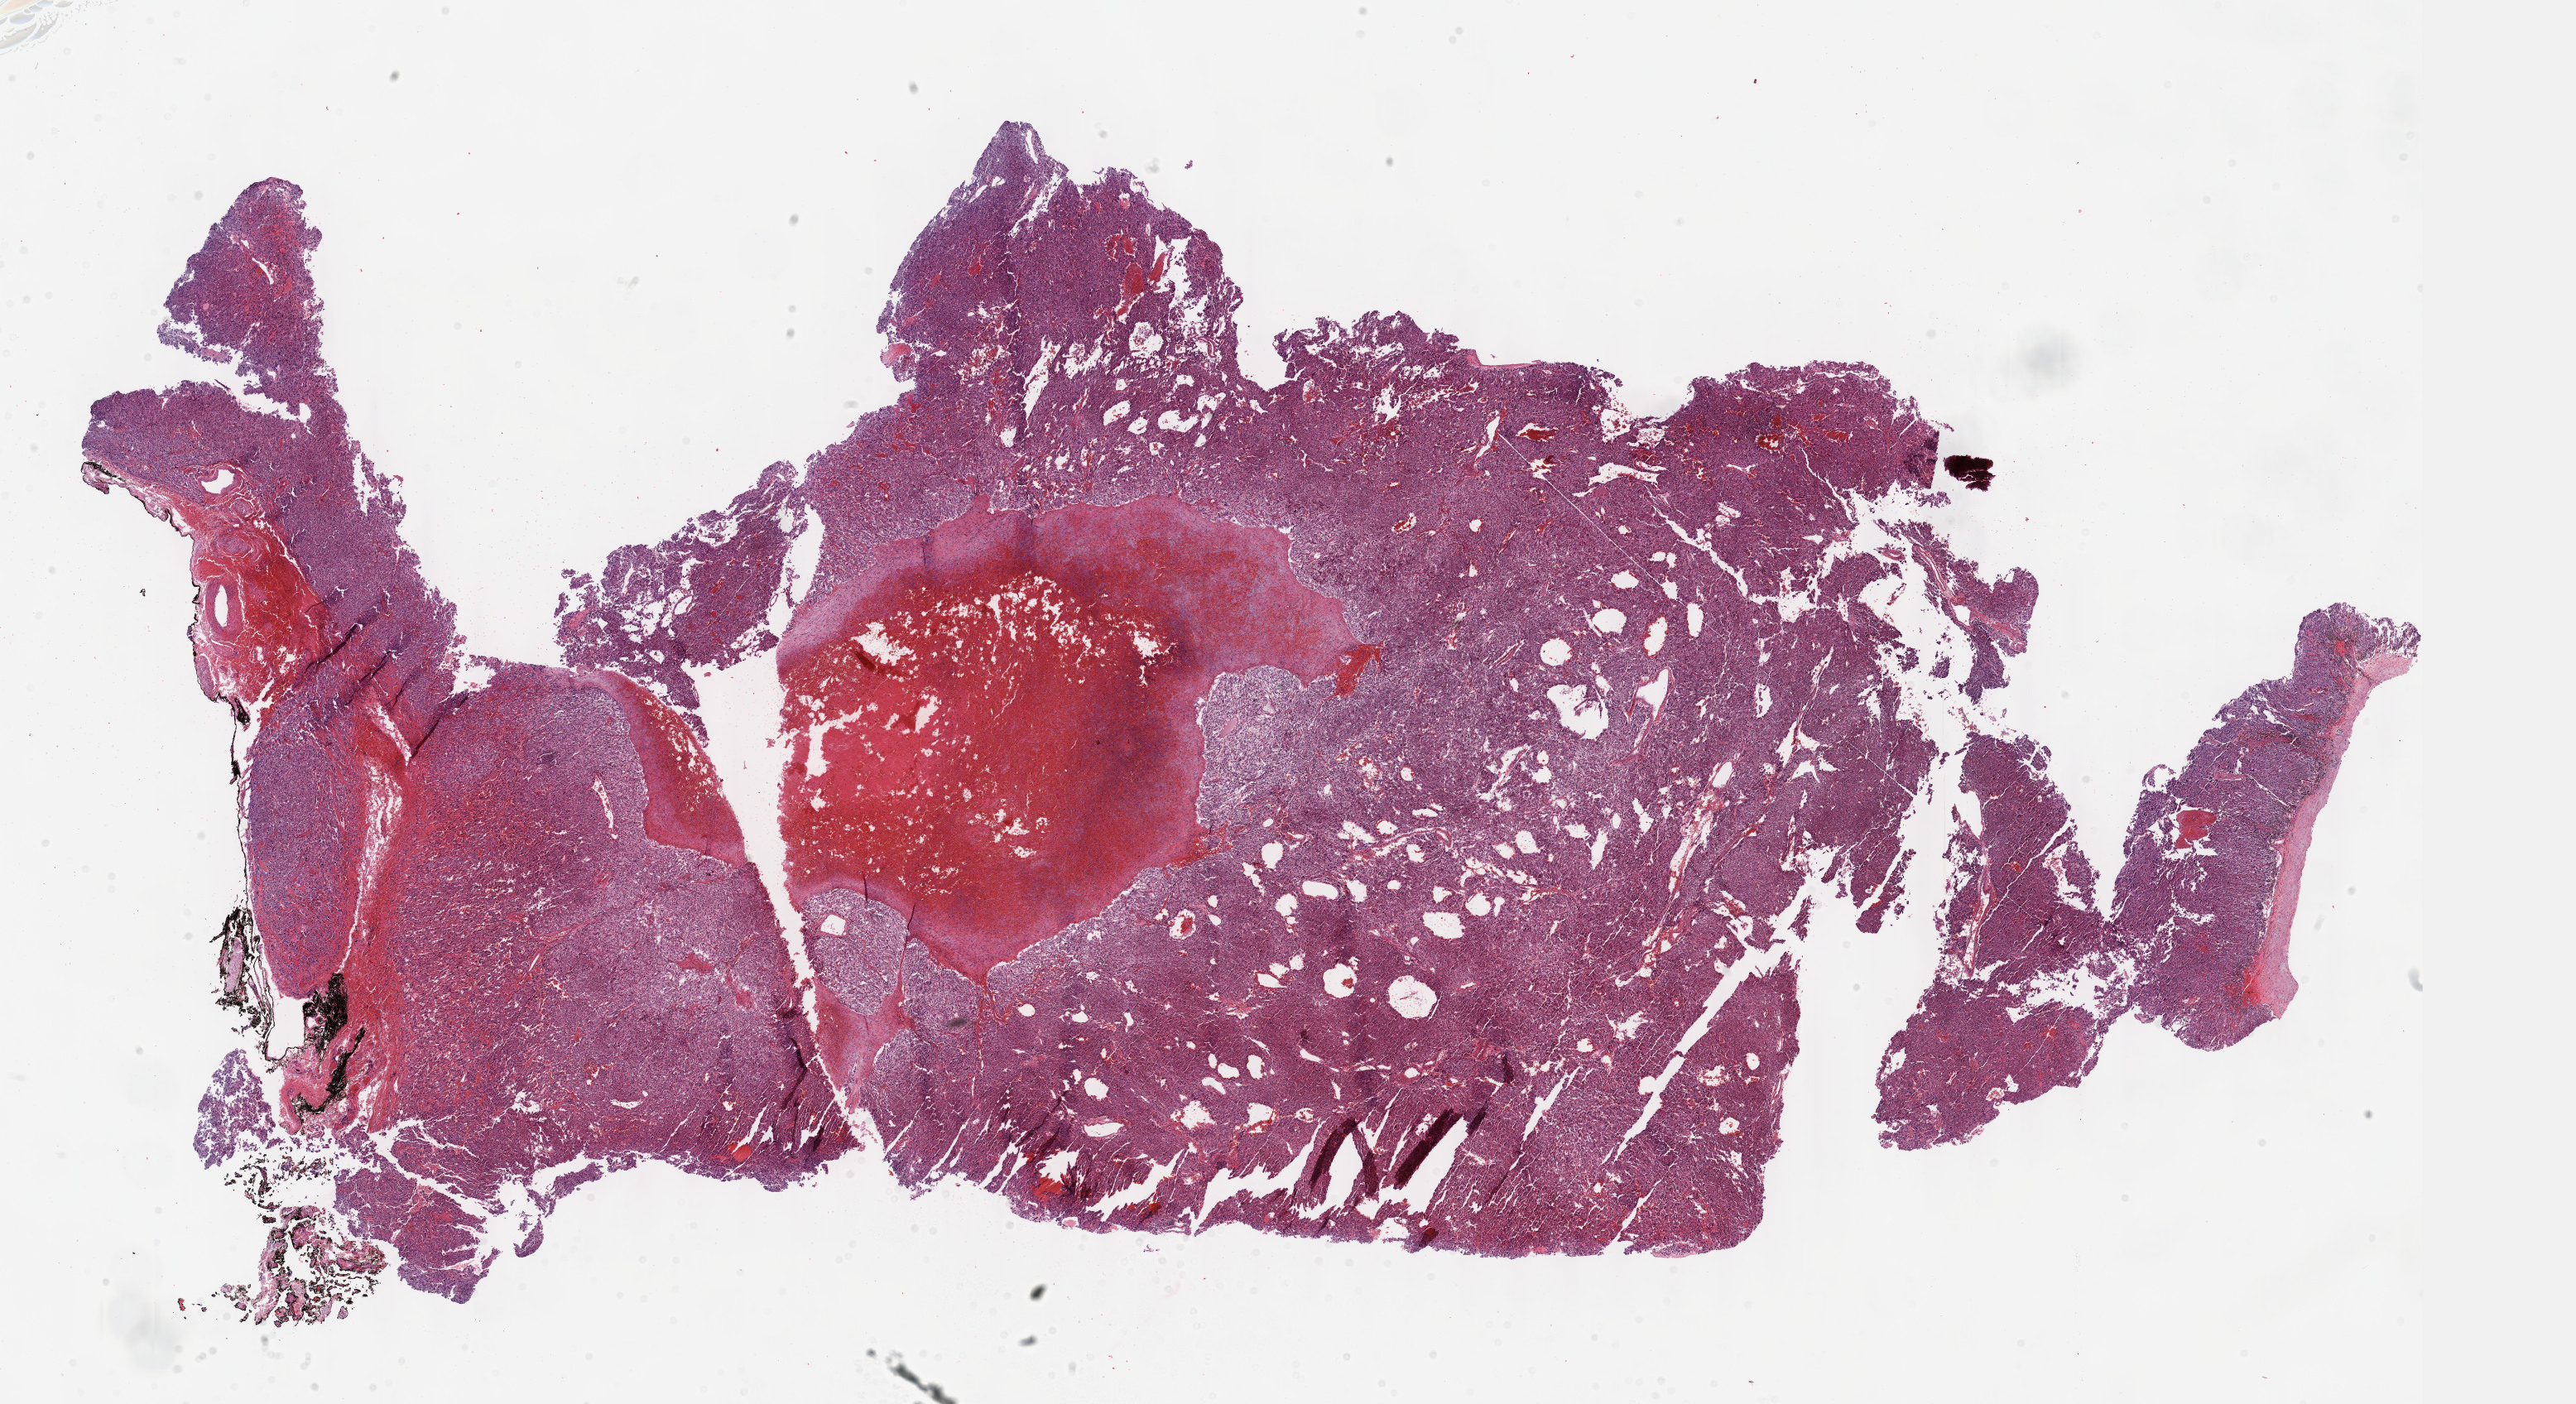
H&E-stained whole-slide image — a low-resolution overview of the entire scanned area, about 25.1 x 13.7 mm. Formalin-fixed paraffin-embedded (FFPE) diagnostic section. Primary tumour sample from the adrenal gland. Patient: female, age at initial diagnosis 35 years.
Histologic diagnosis: Paraganglioma, malignant.